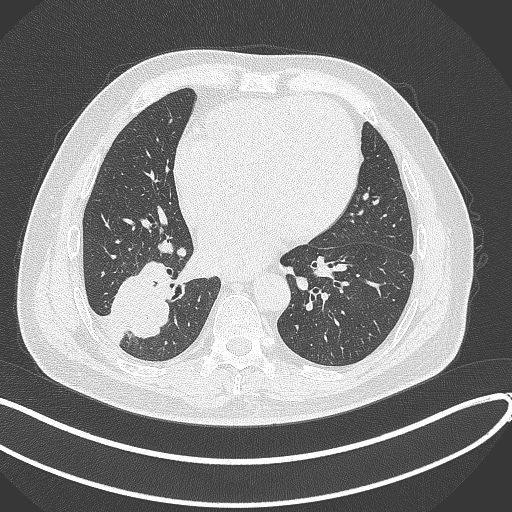
Chest CT, one axial slice; position 142 of 360 along the scan axis; reconstruction kernel B70f; lung window (W 1500 / L -600 HU); 512 × 512 image matrix, field of view 400 × 400 mm. Patient: male, 59 years.
Outlined on this slice (rectangle marked by the reading radiologist):
- lung tumour (recorded histology: adenocarcinoma): bounding box <109,252,175,341> (left, top, right, bottom; pixels)